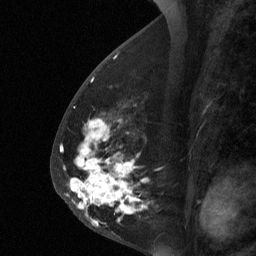
Breast MRI (dynamic contrast-enhanced), one sagittal slice. Position 28 of 64 along the scan axis. Dynamic contrast-enhanced study with each time point stored as its own series, time point 2 of 3 at this slice position (early post-contrast, ordered by acquisition time). 1.5 T. TE 4.8 ms, TR 27 ms. 256 × 256 image matrix, field of view 180 × 180 mm. Patient: female, 56 years. Case-level facts recorded for this patient, not image findings: setting: breast cancer imaged before/during neoadjuvant chemotherapy; receptor status: HER2-positive.
Structures marked on this image (semi-automatically segmented with operator editing):
- analysis volume of interest (the breast-tissue region the enhancement analysis was run in; not a lesion): bounding box (x1, y1, x2, y2) in pixels: (59, 104, 153, 229)
- tumour enhancement mask (voxels above the 90 % enhancement threshold inside the analysis volume of interest): (69, 146, 138, 226)